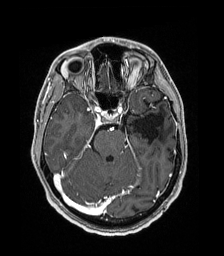
Brain MRI from a brain-tumour surgery series, one axial slice. Slice 119 of 192 in the series (ordered by position). T1-weighted post-contrast. 1 mm slice thickness. 224 × 256 image matrix. Case-level facts recorded for this patient, not image findings: histopathology: Low grade glioma; IDH mutation: no; tumour location: Left Parieto-Occipital Intraventricular.
Annotated regions visible in this slice (expert manual segmentation):
- previous resection cavity: bounding box (x1, y1, x2, y2) in pixels: (133, 113, 163, 144)